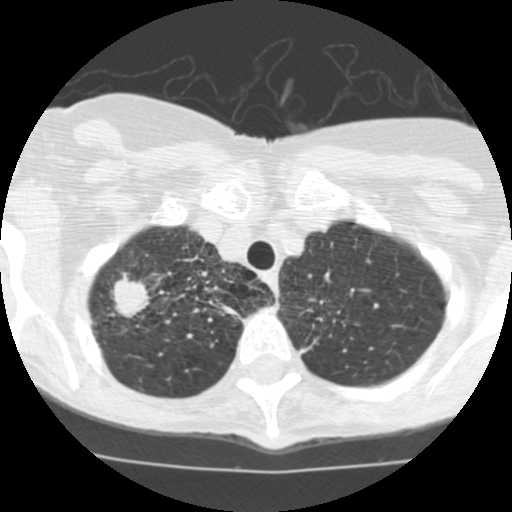
Low-dose screening chest CT, axial slice, second screening round (one year after baseline), lung window (W 1500 / L -600 HU), 2.5 mm slice thickness, standard (soft-tissue) reconstruction kernel (STANDARD), slice 18 of 115 in the series. Female participant, aged 68 years at enrolment.
- Expert reader's lesion annotation, bounding box <92,265,158,336> (left, top, right, bottom; pixels).
- The screening reader recorded 3 non-calcified nodules or masses ≥4 mm on this exam (right upper lobe, right upper lobe, right middle lobe); which of them this box marks is not recorded.
- Official screen result: positive, other.
- Participant outcome: lung cancer diagnosed 36 days after this screen — large cell neuroendocrine carcinoma, right upper lobe, undifferentiated (G4), stage IB (AJCC 6th edition), 22 mm at pathology.